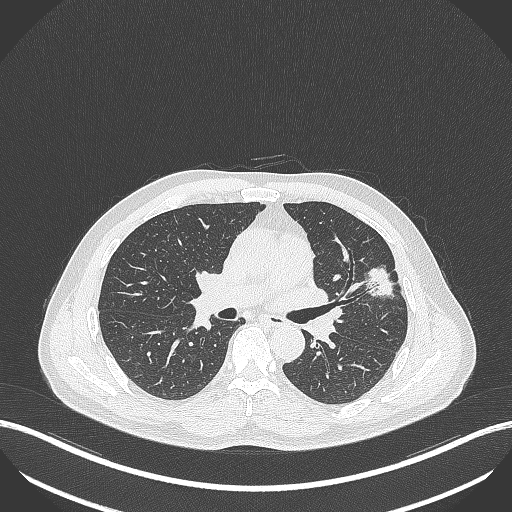
Chest CT, one axial slice; position 225 of 418 along the scan axis; 120 kVp; lung window (W 1500 / L -600 HU); 512 × 512 image matrix, field of view 400 × 400 mm. Patient: male, 55 years. Case-level facts recorded for this patient, not image findings: clinical TNM (as recorded): T1c N0 M0; histopathological grade: G2-3.
Annotated regions visible in this slice (rectangle marked by the reading radiologist):
- lung tumour (recorded histology: adenocarcinoma): bounding box [x1, y1, x2, y2] px = [360, 261, 398, 300]